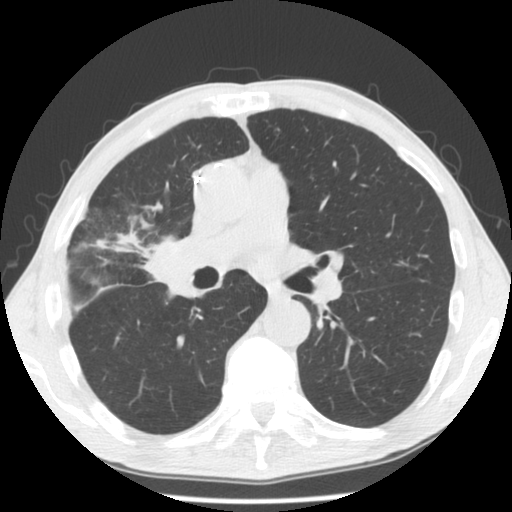
Chest CT (low-dose screening protocol), one axial image. Third screening round (two years after baseline). Lung window (W 1500 / L -600 HU). 2.5 mm slice thickness. Standard (soft-tissue) reconstruction kernel (STANDARD). Slice 74 of 132 in the series. 512 × 512 image matrix. Male, age 57 years at enrolment. Former smoker at enrolment.
Lesion marked by an expert reader, box from (x=56, y=201) to (x=165, y=298) px. Screening reader's record for this exam (one nodule recorded; not confirmed to be the boxed lesion): non-calcified nodule or mass ≥4 mm, right upper lobe, 38 × 34 mm, poorly defined margins, mixed attenuation, pre-existing on the prior screen: no. Official screen result: positive, other.